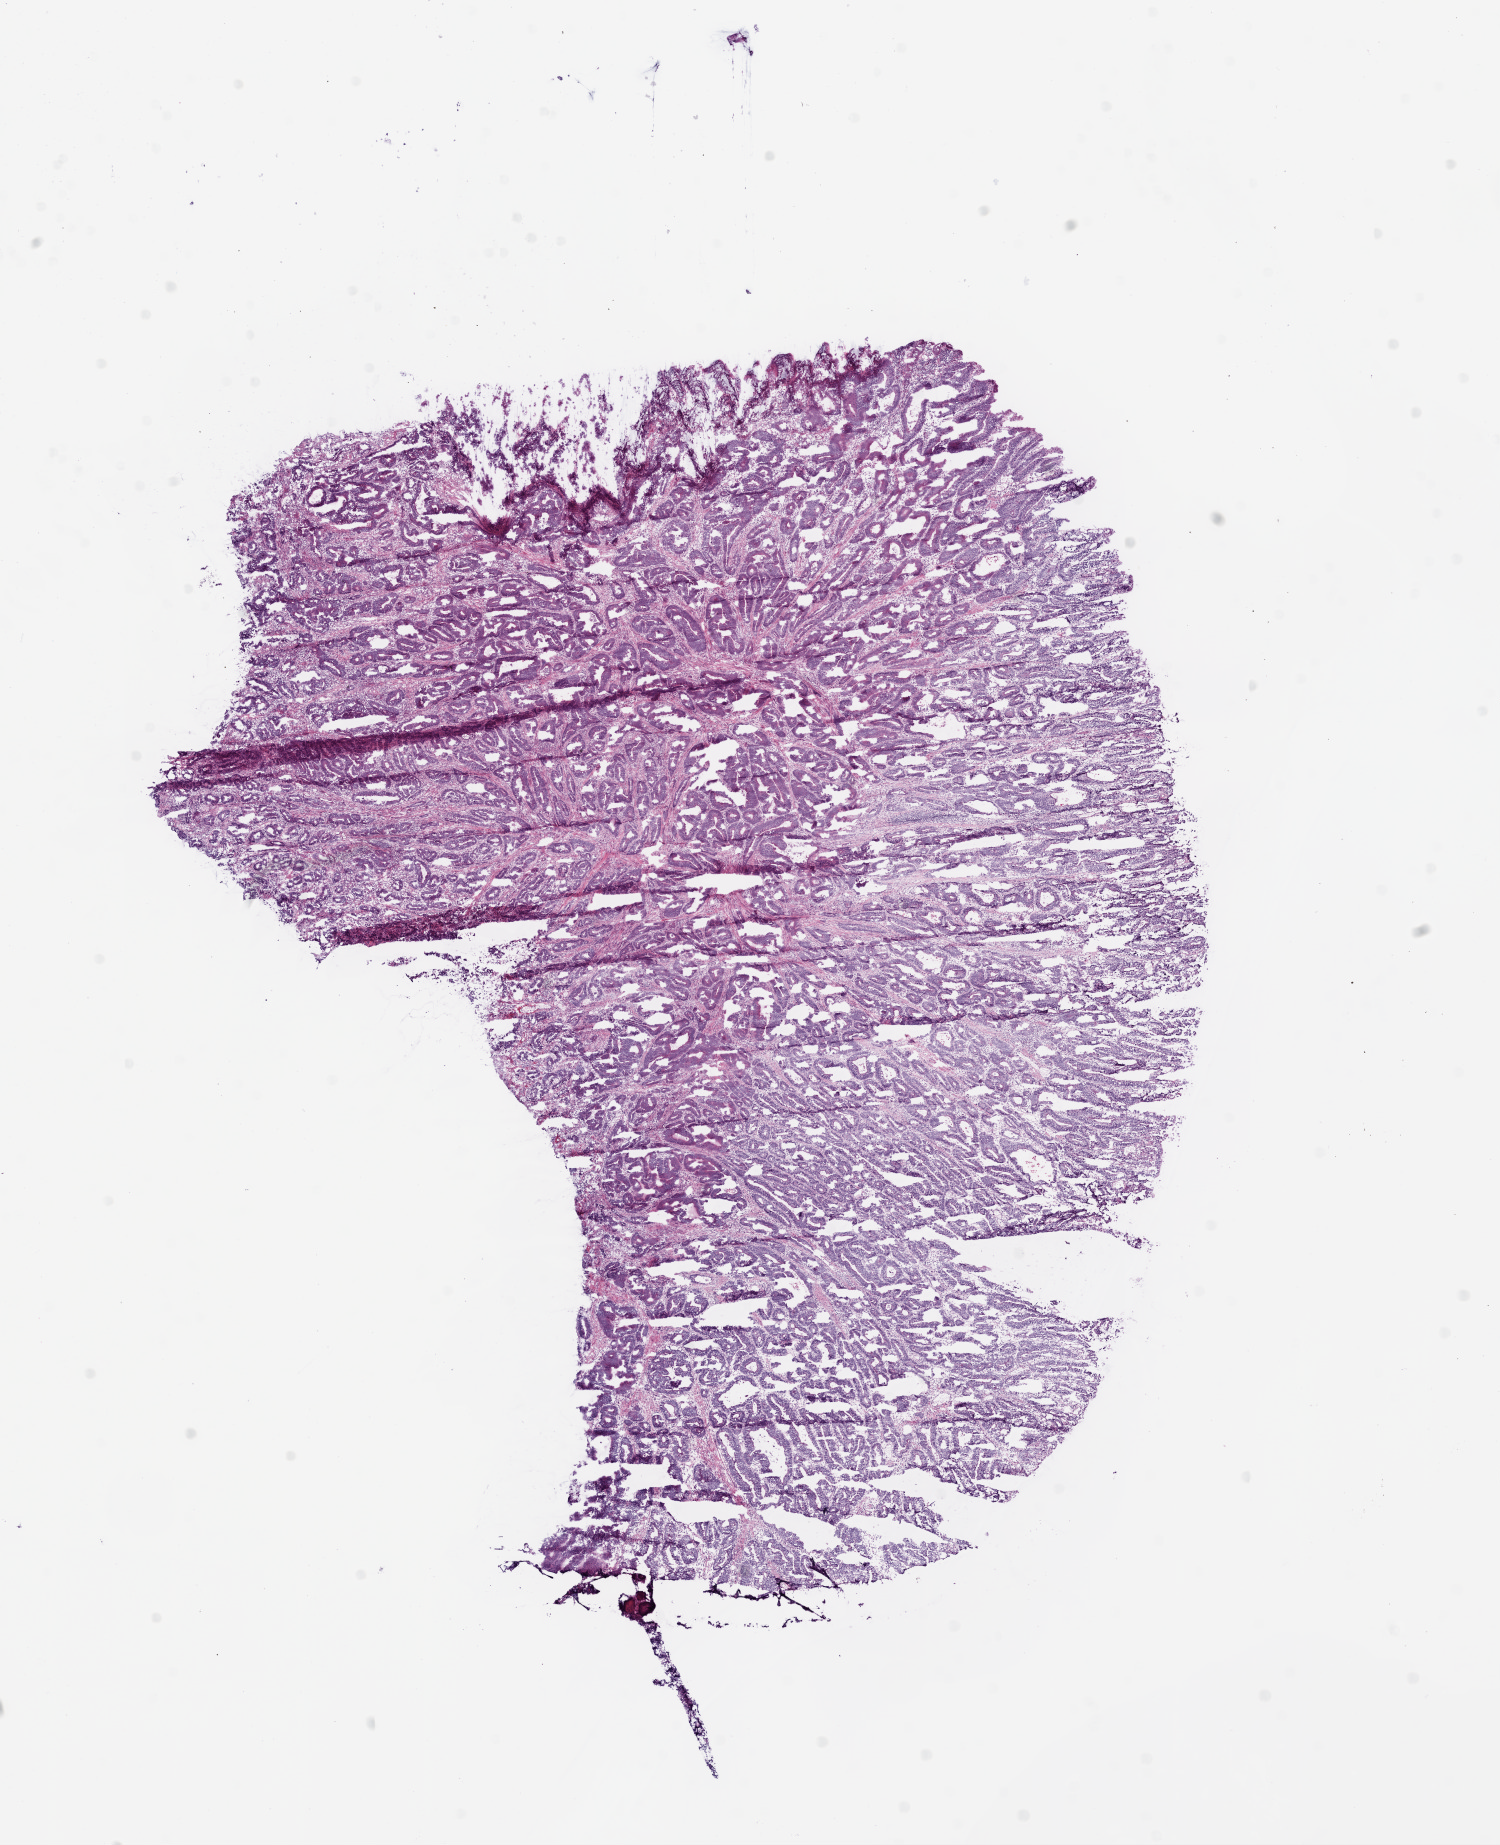
Digitized Hematoxylin and eosin (H&E) stained tissue section (whole slide), low-resolution overview of the scanned area, about 12.0 x 14.8 mm; frozen section; sample: primary tumour, rectum. Male patient; age at initial diagnosis 68 years. Slide review estimates, as recorded: tumour cells 82%, tumour nuclei 80%, normal cells 0%, stromal cells 8%, necrosis 10%.
Lymph nodes positive (case pathology): 0 of 32 examined. AJCC pathologic stage: IIA. TNM: T3 N0 M0. Diagnosis: Adenocarcinoma, NOS.